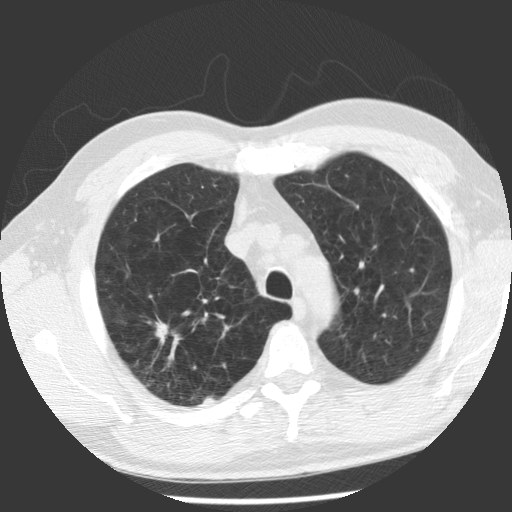
Axial slice from a low-dose chest CT screening exam. Baseline screening round. Lung window (W 1500 / L -600 HU). Standard (soft-tissue) reconstruction kernel (STANDARD). Slice 87 of 112 in the series. 512 × 512 image matrix, field of view 344 × 344 mm. Male, age 62 years at enrolment. Former smoker at enrolment.
Expert reader's lesion annotation, box from (x=118, y=302) to (x=197, y=381) px. The screening reader recorded 2 non-calcified nodules or masses ≥4 mm on this exam; which of them this box marks is not recorded. Official screen result: positive, change unspecified: nodule(s) >= 4 mm or enlarging nodule(s), mass(es), or other non-specific abnormalities suspicious for lung cancer. Lung cancer was diagnosed 71 days after this screen: adenocarcinoma, NOS, right upper lobe, poorly differentiated (G3), stage IV (AJCC 6th edition), 30 mm at pathology.